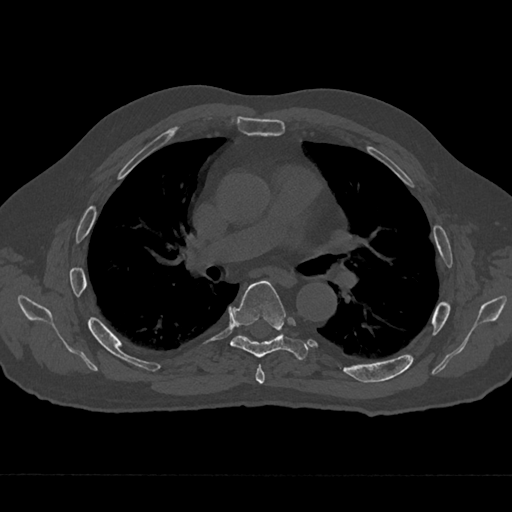
CT including the spine, one axial slice; slice 423 of 797 in the series (ordered by position); reconstruction kernel Br40s/3; bone window (W 1800 / L 400 HU); 0.5 mm slice thickness; 512 × 512 image matrix, field of view 377 × 377 mm. Patient: male, 75 years. From the clinical record (not read from this slice): primary cancer: renal; vertebrae with lytic lesions (as recorded): T4.
Outlined on this slice (semi-automatically segmented with operator editing):
- T5 vertebra: bounding box [x1, y1, x2, y2] px = [255, 365, 265, 384]
- T6 vertebra: [230, 281, 308, 360]